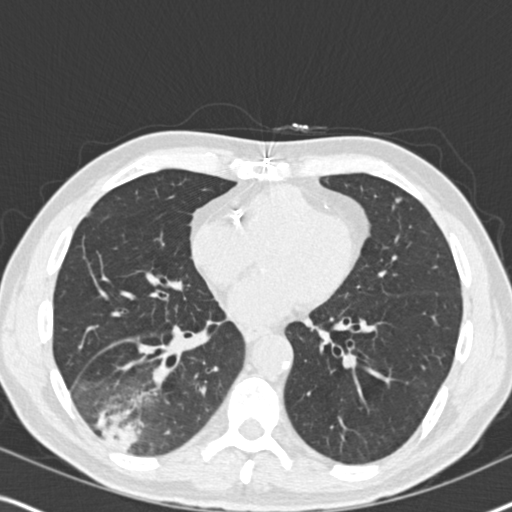
Low-dose screening chest CT, one axial slice; 120 kVp; lung window (W 1500 / L -600 HU); 2 mm slice thickness; 512 × 512 image matrix, field of view 330 × 330 mm.
Outlined on this slice (outlined manually by an expert reader):
- lesion 1 (tumor, lower lobe of right lung): box from (x=100, y=418) to (x=139, y=450) px